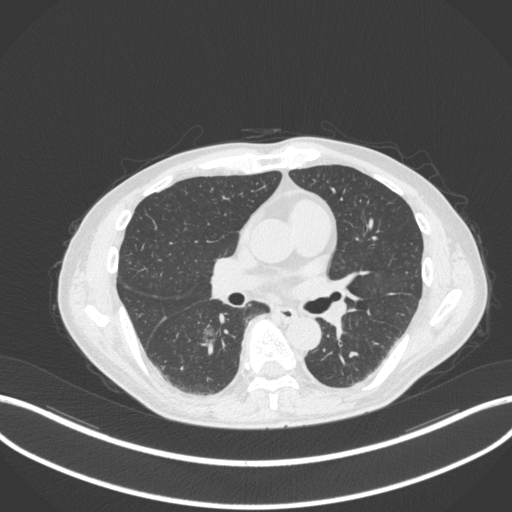
Chest CT, one axial slice; slice 172 of 324 in the series (ordered by position); reconstruction kernel B31f; 120 kVp; lung window (W 1500 / L -600 HU); 1 mm slice thickness; 512 × 512 image matrix, field of view 400 × 400 mm. Male patient, age 61 years. Case-level facts recorded for this patient, not image findings: clinical TNM (as recorded): T1c N0 M0.
Annotated regions visible in this slice (bounding box drawn by a radiologist):
- lung tumour (recorded histology: adenocarcinoma): box from (x=200, y=318) to (x=219, y=355) px